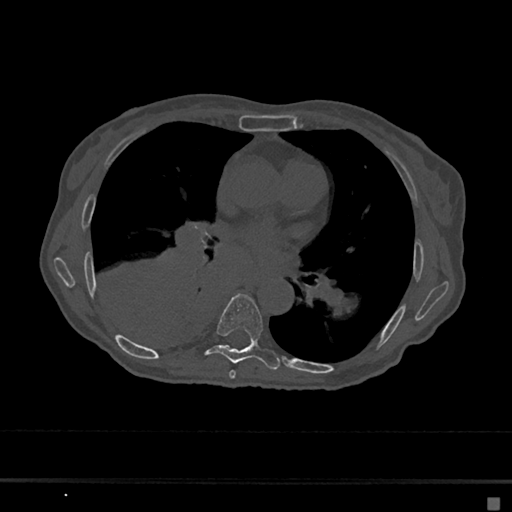
CT including the spine, one axial slice. Reconstruction kernel Br40s/3. Bone window (W 1800 / L 400 HU). 0.5 mm slice thickness. 512 × 512 image matrix, field of view 360 × 360 mm. Patient: female, 68 years. Case-level facts recorded for this patient, not image findings: primary cancer: renal.
Annotated regions visible in this slice (semi-automatic segmentation, software-assisted and operator-edited):
- T6 vertebra: bounding box [x1, y1, x2, y2] px = [229, 370, 236, 379]
- T7 vertebra: [205, 294, 280, 370]